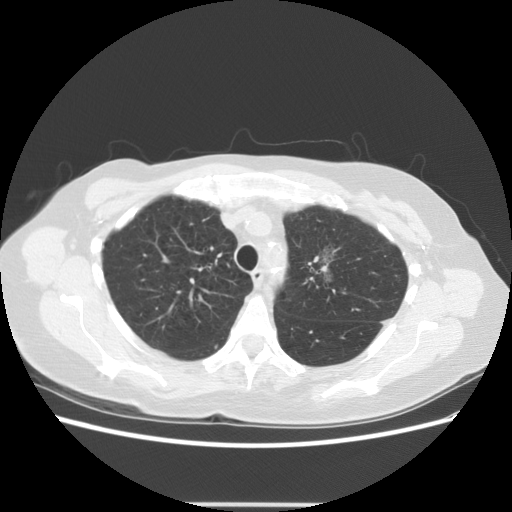
Axial slice from a low-dose chest CT screening exam, third screening round (two years after baseline), lung window (W 1500 / L -600 HU), standard (soft-tissue) reconstruction kernel (STANDARD), 140 kVp. Female participant, aged 65 years at enrolment. Former smoker at enrolment.
• Expert-annotated lung lesion, bounding box <291,222,372,294> (left, top, right, bottom; pixels).
• Reader record for this screening exam (exam-level; its link to the box is not recorded): non-calcified nodule or mass ≥4 mm, left upper lobe, 17 × 14 mm, poorly defined margins, ground glass attenuation, pre-existing on the prior screen: yes; interval growth: yes.
• Official screen result: positive, other.
• Later outcome: lung cancer diagnosed 96 days after this screen — adenocarcinoma, NOS, left upper lobe, moderately differentiated (G2), stage IA (AJCC 6th edition), 30 mm at pathology.